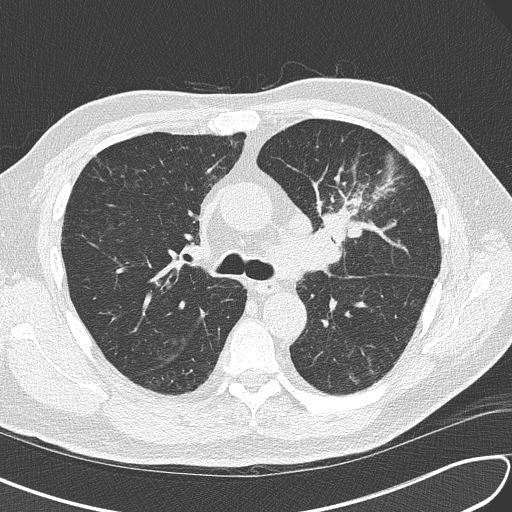
Chest CT (low-dose screening protocol), one axial image, third screening round (two years after baseline), lung window (W 1500 / L -600 HU), 120 kVp. Male, age 67 years at enrolment. Current smoker at enrolment.
- Expert-annotated lung lesion, bounding box <297,172,398,266> (left, top, right, bottom; pixels).
- Screening reader's record for this exam (one nodule recorded; not confirmed to be the boxed lesion): non-calcified nodule or mass ≥4 mm, left upper lobe, 30 × 23 mm, soft tissue attenuation, pre-existing on the prior screen: no.
- Lung cancer was diagnosed 41 days after this screen: small cell carcinoma, NOS, left upper lobe, stage IV (AJCC 6th edition), 30 mm at pathology.